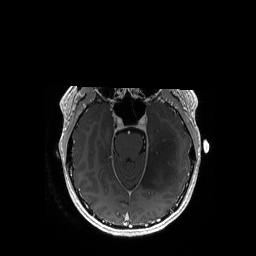
Brain MRI from a brain-tumour surgery series, one axial slice; position 115 of 192 along the scan axis; T1-weighted post-contrast; 1 mm slice thickness; 256 × 256 image matrix. Case-level facts recorded for this patient, not image findings: histopathology: Astrocytoma; WHO grade: 3; IDH mutation: yes.
Annotated regions visible in this slice (manually delineated by an expert):
- tumour: bounding box (x1, y1, x2, y2) in pixels: (142, 115, 178, 190)